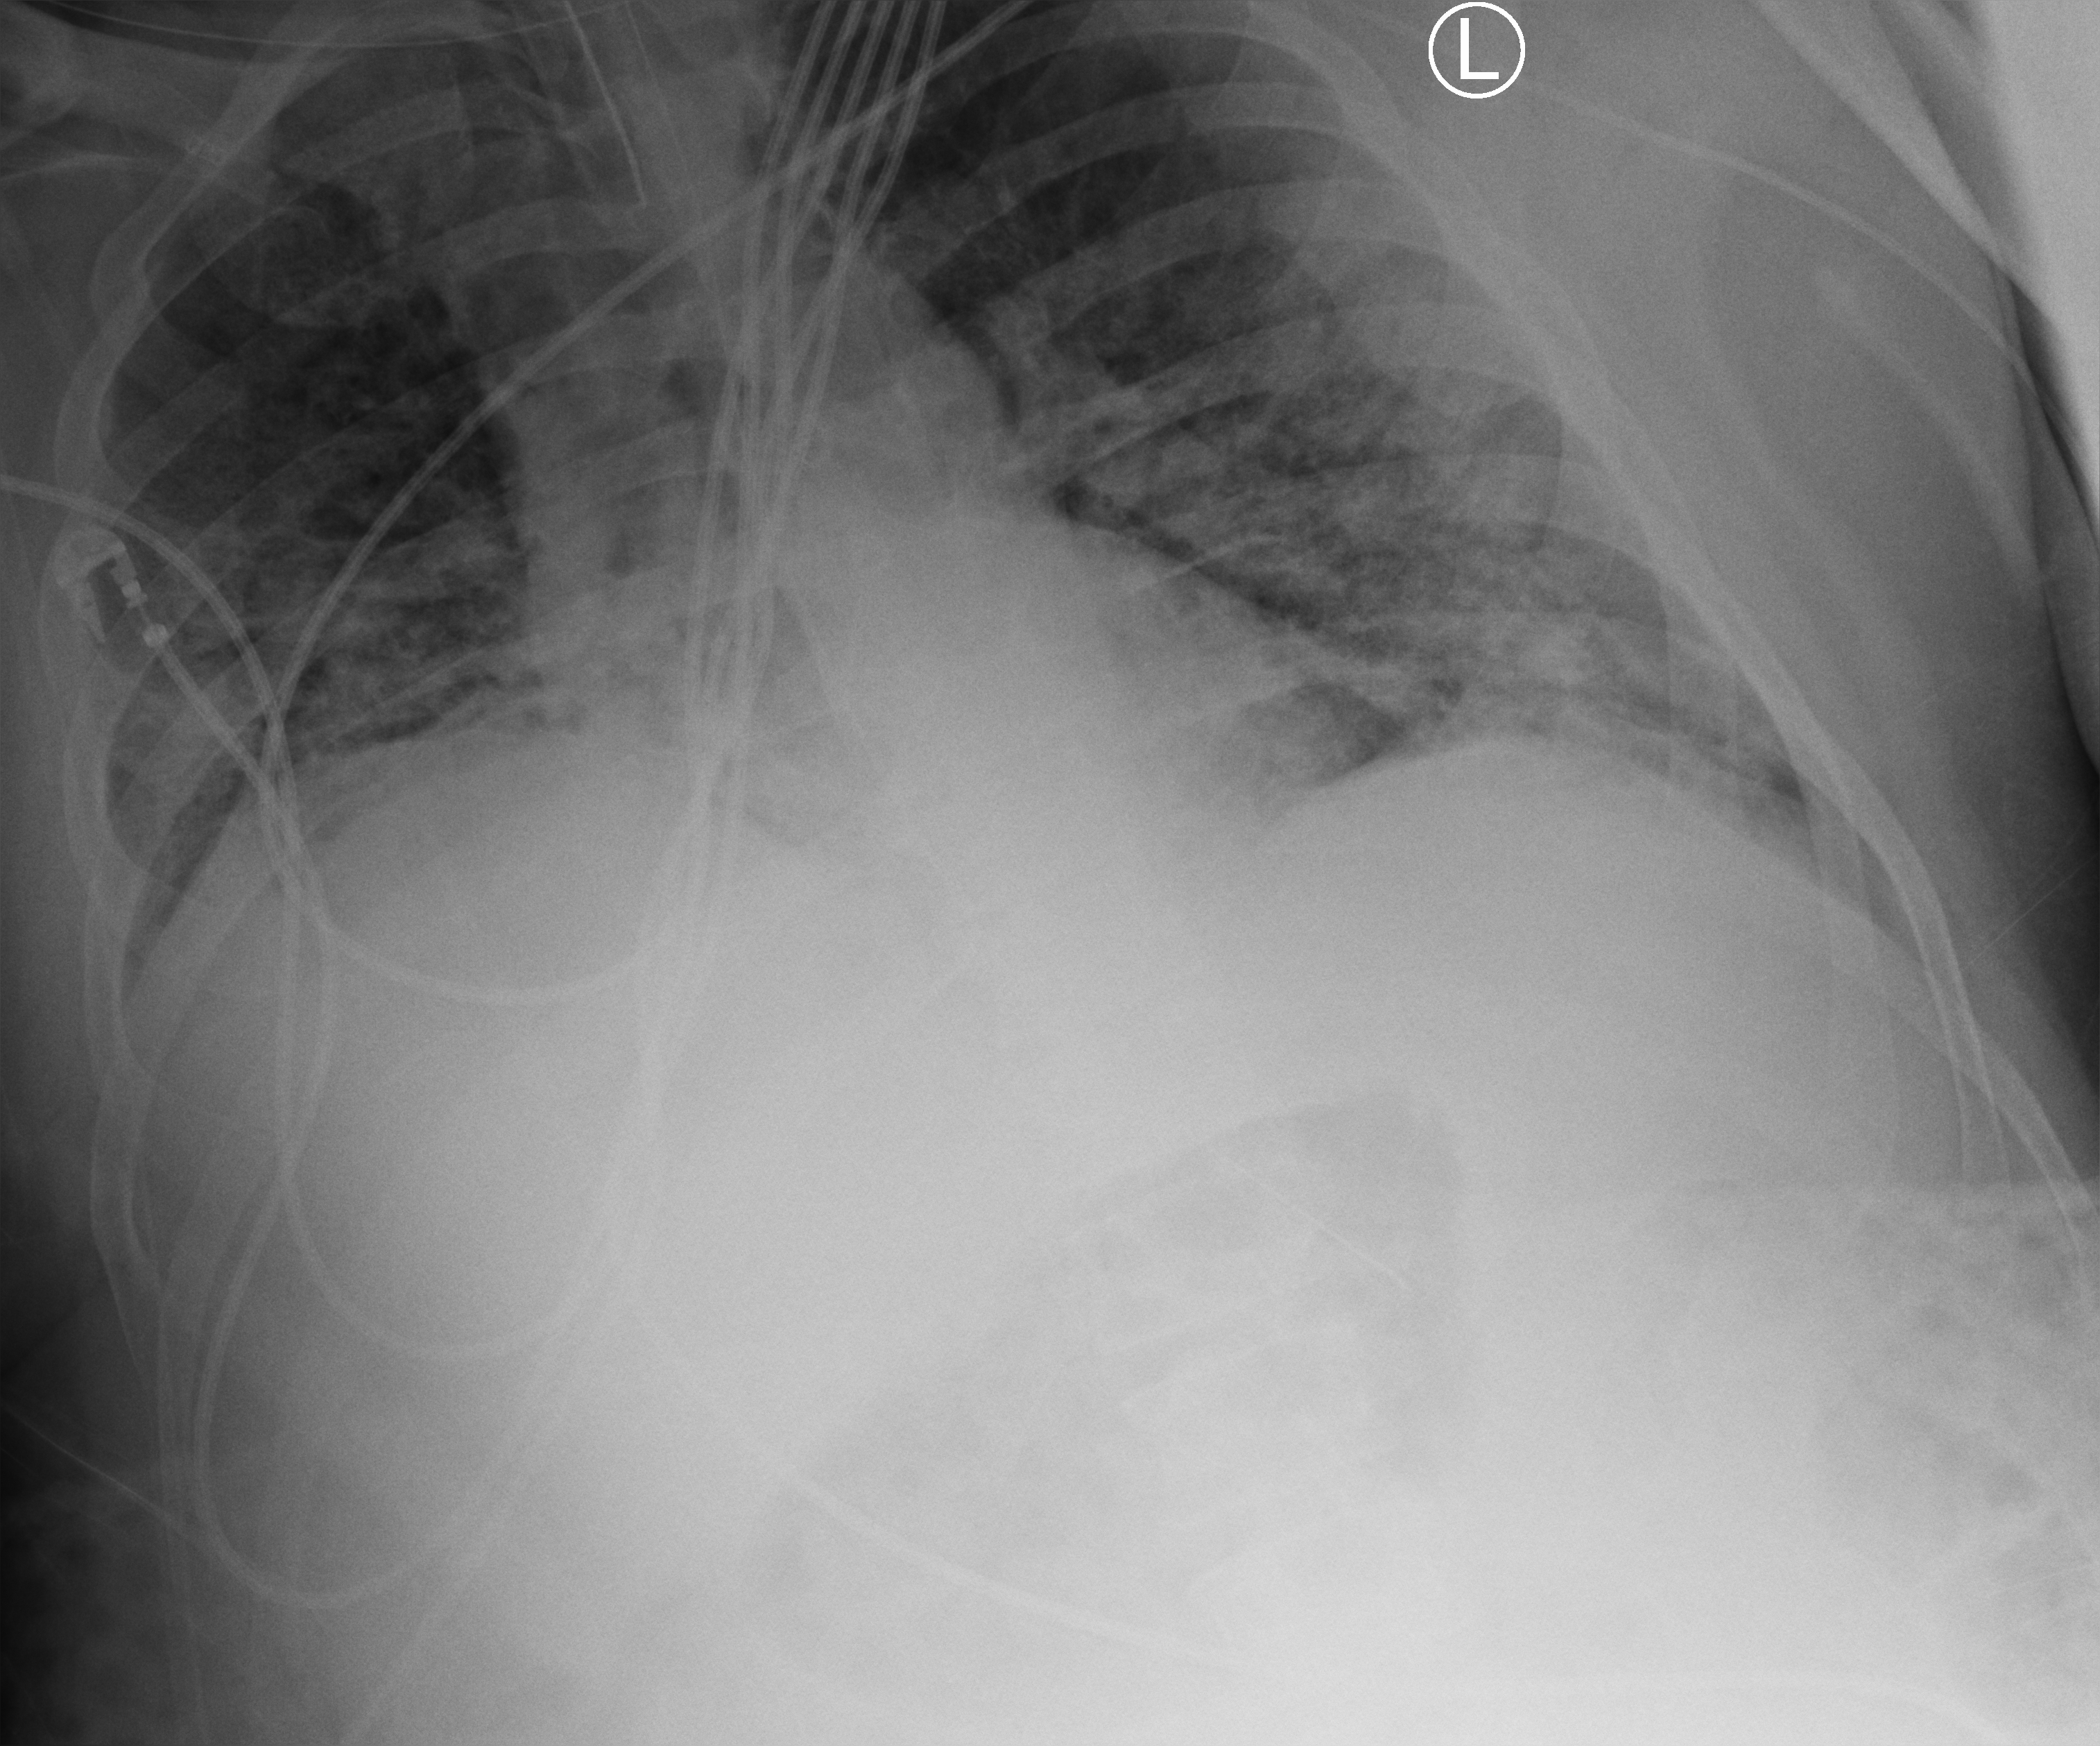
Bedside chest radiograph (computed radiography); anteroposterior (AP) projection. Male patient hospitalised with COVID-19, age 18–59 years.
From the hospital-stay record, not from the radiograph (when in the stay this image was taken is not recorded):
- smoking status (admission record): never
- admitted to intensive care during this hospital stay: yes